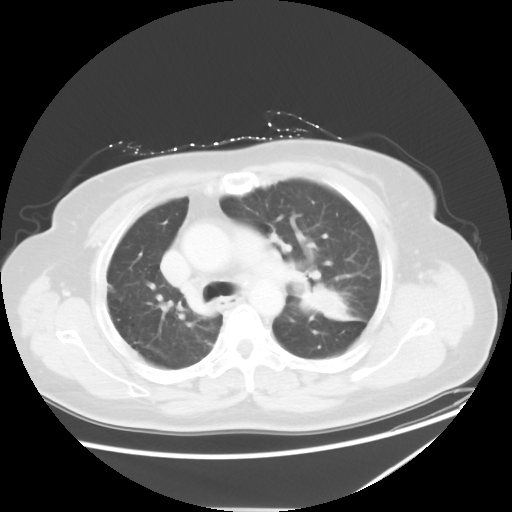
Chest CT, one axial slice. Slice 38 of 54 in the series (ordered by position). 120 kVp. Lung window (W 1500 / L -600 HU). 5 mm slice thickness. 512 × 512 image matrix, field of view 384 × 384 mm. Patient: female, 61 years. From the clinical record (not read from this slice): clinical TNM (as recorded): T1c N3 M1.
Structures marked on this image (bounding box drawn by a radiologist):
- lung tumour (recorded histology: adenocarcinoma): box from (x=301, y=282) to (x=369, y=328) px